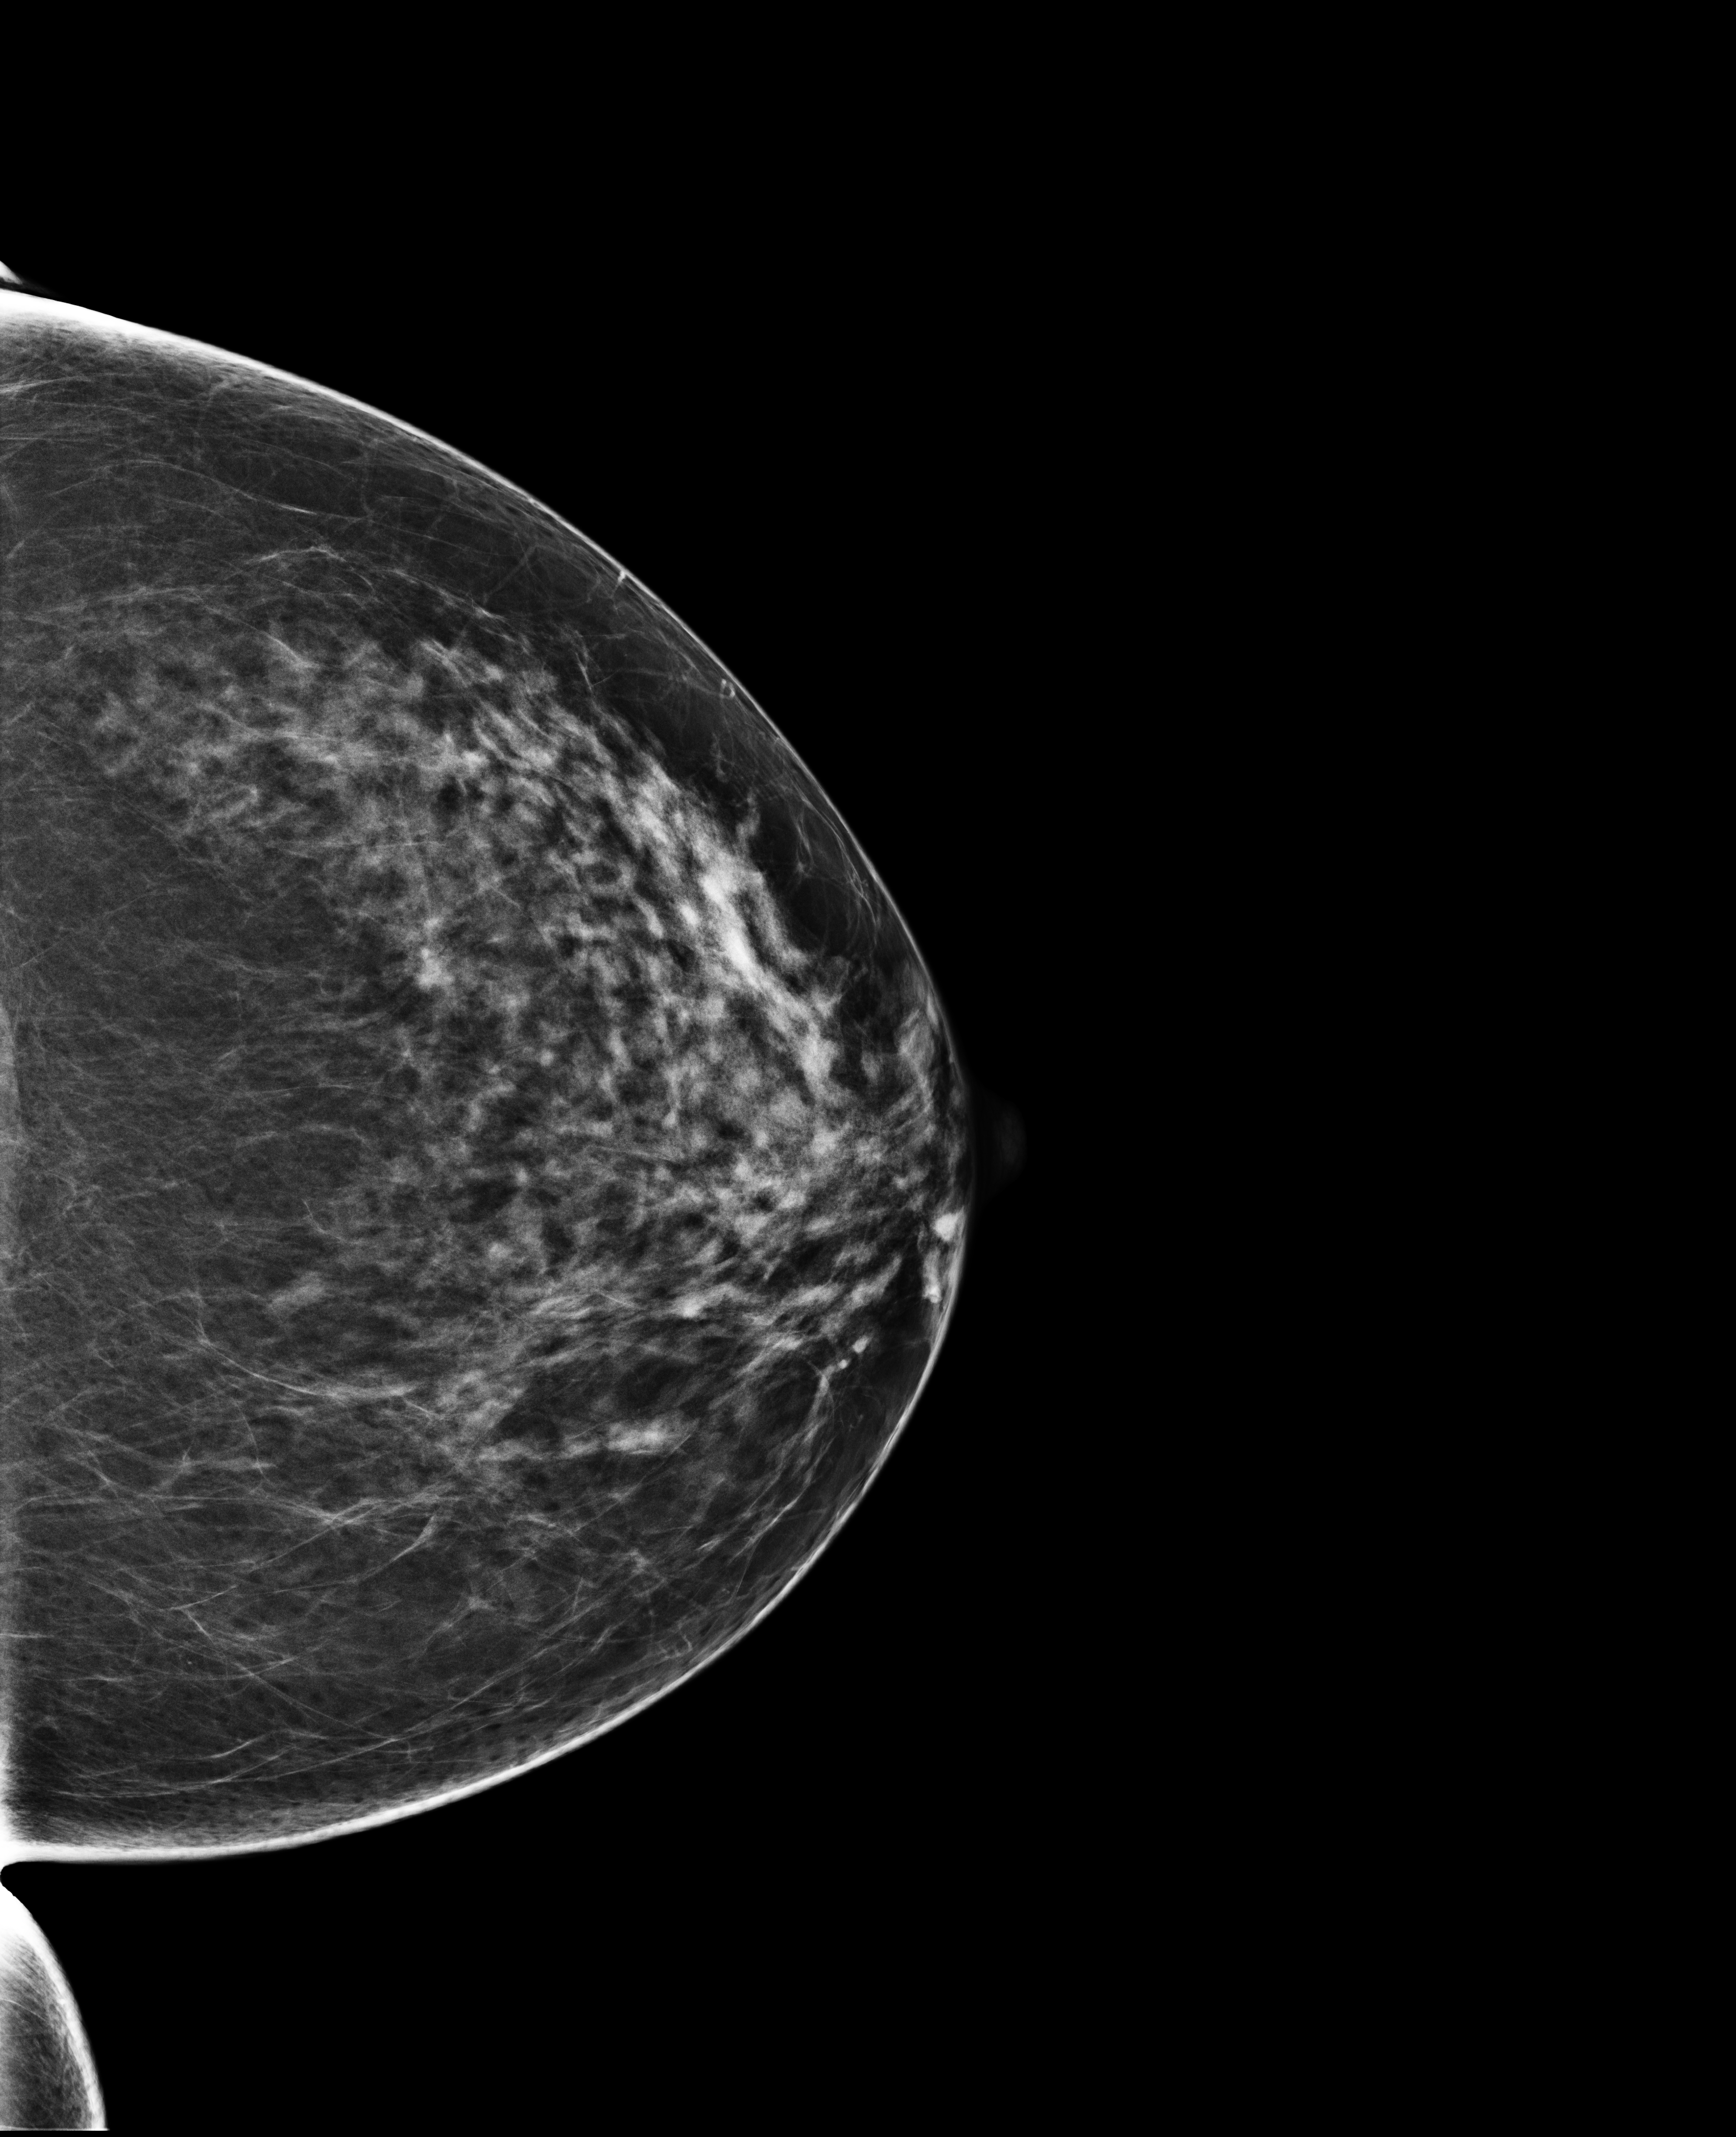
Digital mammogram (FFDM); left breast; CC view; annual screening mammography examination; compressed breast thickness 76 mm. Female patient, age 52 years.
BI-RADS breast density category at the screening exam (both breasts, scale 1–4): 3. Final BI-RADS assessment for this screening round (tomosynthesis exam, both breasts): category 1. Recall: no recall after this screen.